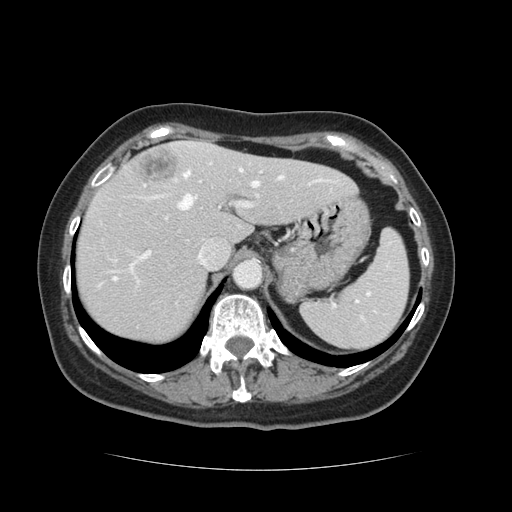
Contrast-enhanced abdominal CT, one axial slice. Position 93 of 128 along the scan axis. Intravenous contrast given. Soft-tissue window (W 400 / L 40 HU). 2.5 mm slice thickness. 512 × 512 image matrix, field of view 366 × 366 mm. Female patient, age 67 years. From the clinical record (not read from this slice): diagnosis: colorectal cancer liver metastases, imaged before liver resection; multiple liver metastases: yes.
Structures marked on this image (expert manual segmentation):
- hepatic veins: box from (x=114, y=168) to (x=284, y=284) px
- liver: (x=75, y=143)–(x=353, y=343)
- planned liver remnant (the part of the liver to remain after resection): (x=75, y=157)–(x=353, y=343)
- portal vein (with intrahepatic branches): (x=143, y=161)–(x=262, y=258)
- liver metastasis: (x=135, y=151)–(x=181, y=183)